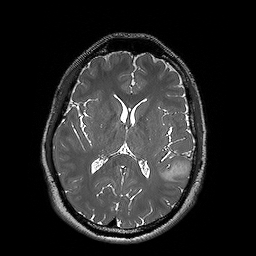
Brain MRI from a brain-tumour surgery series, one axial slice; slice 82 of 192 in the series (ordered by position); 1 mm slice thickness; 256 × 256 image matrix, field of view 250 × 250 mm. From the clinical record (not read from this slice): histopathology: Oligodendroglioma; WHO grade: 2; IDH mutation: yes; tumour location: Left Posterior Temporal.
Outlined on this slice (manually delineated by an expert):
- tumour: bounding box <159,161,193,181> (left, top, right, bottom; pixels)